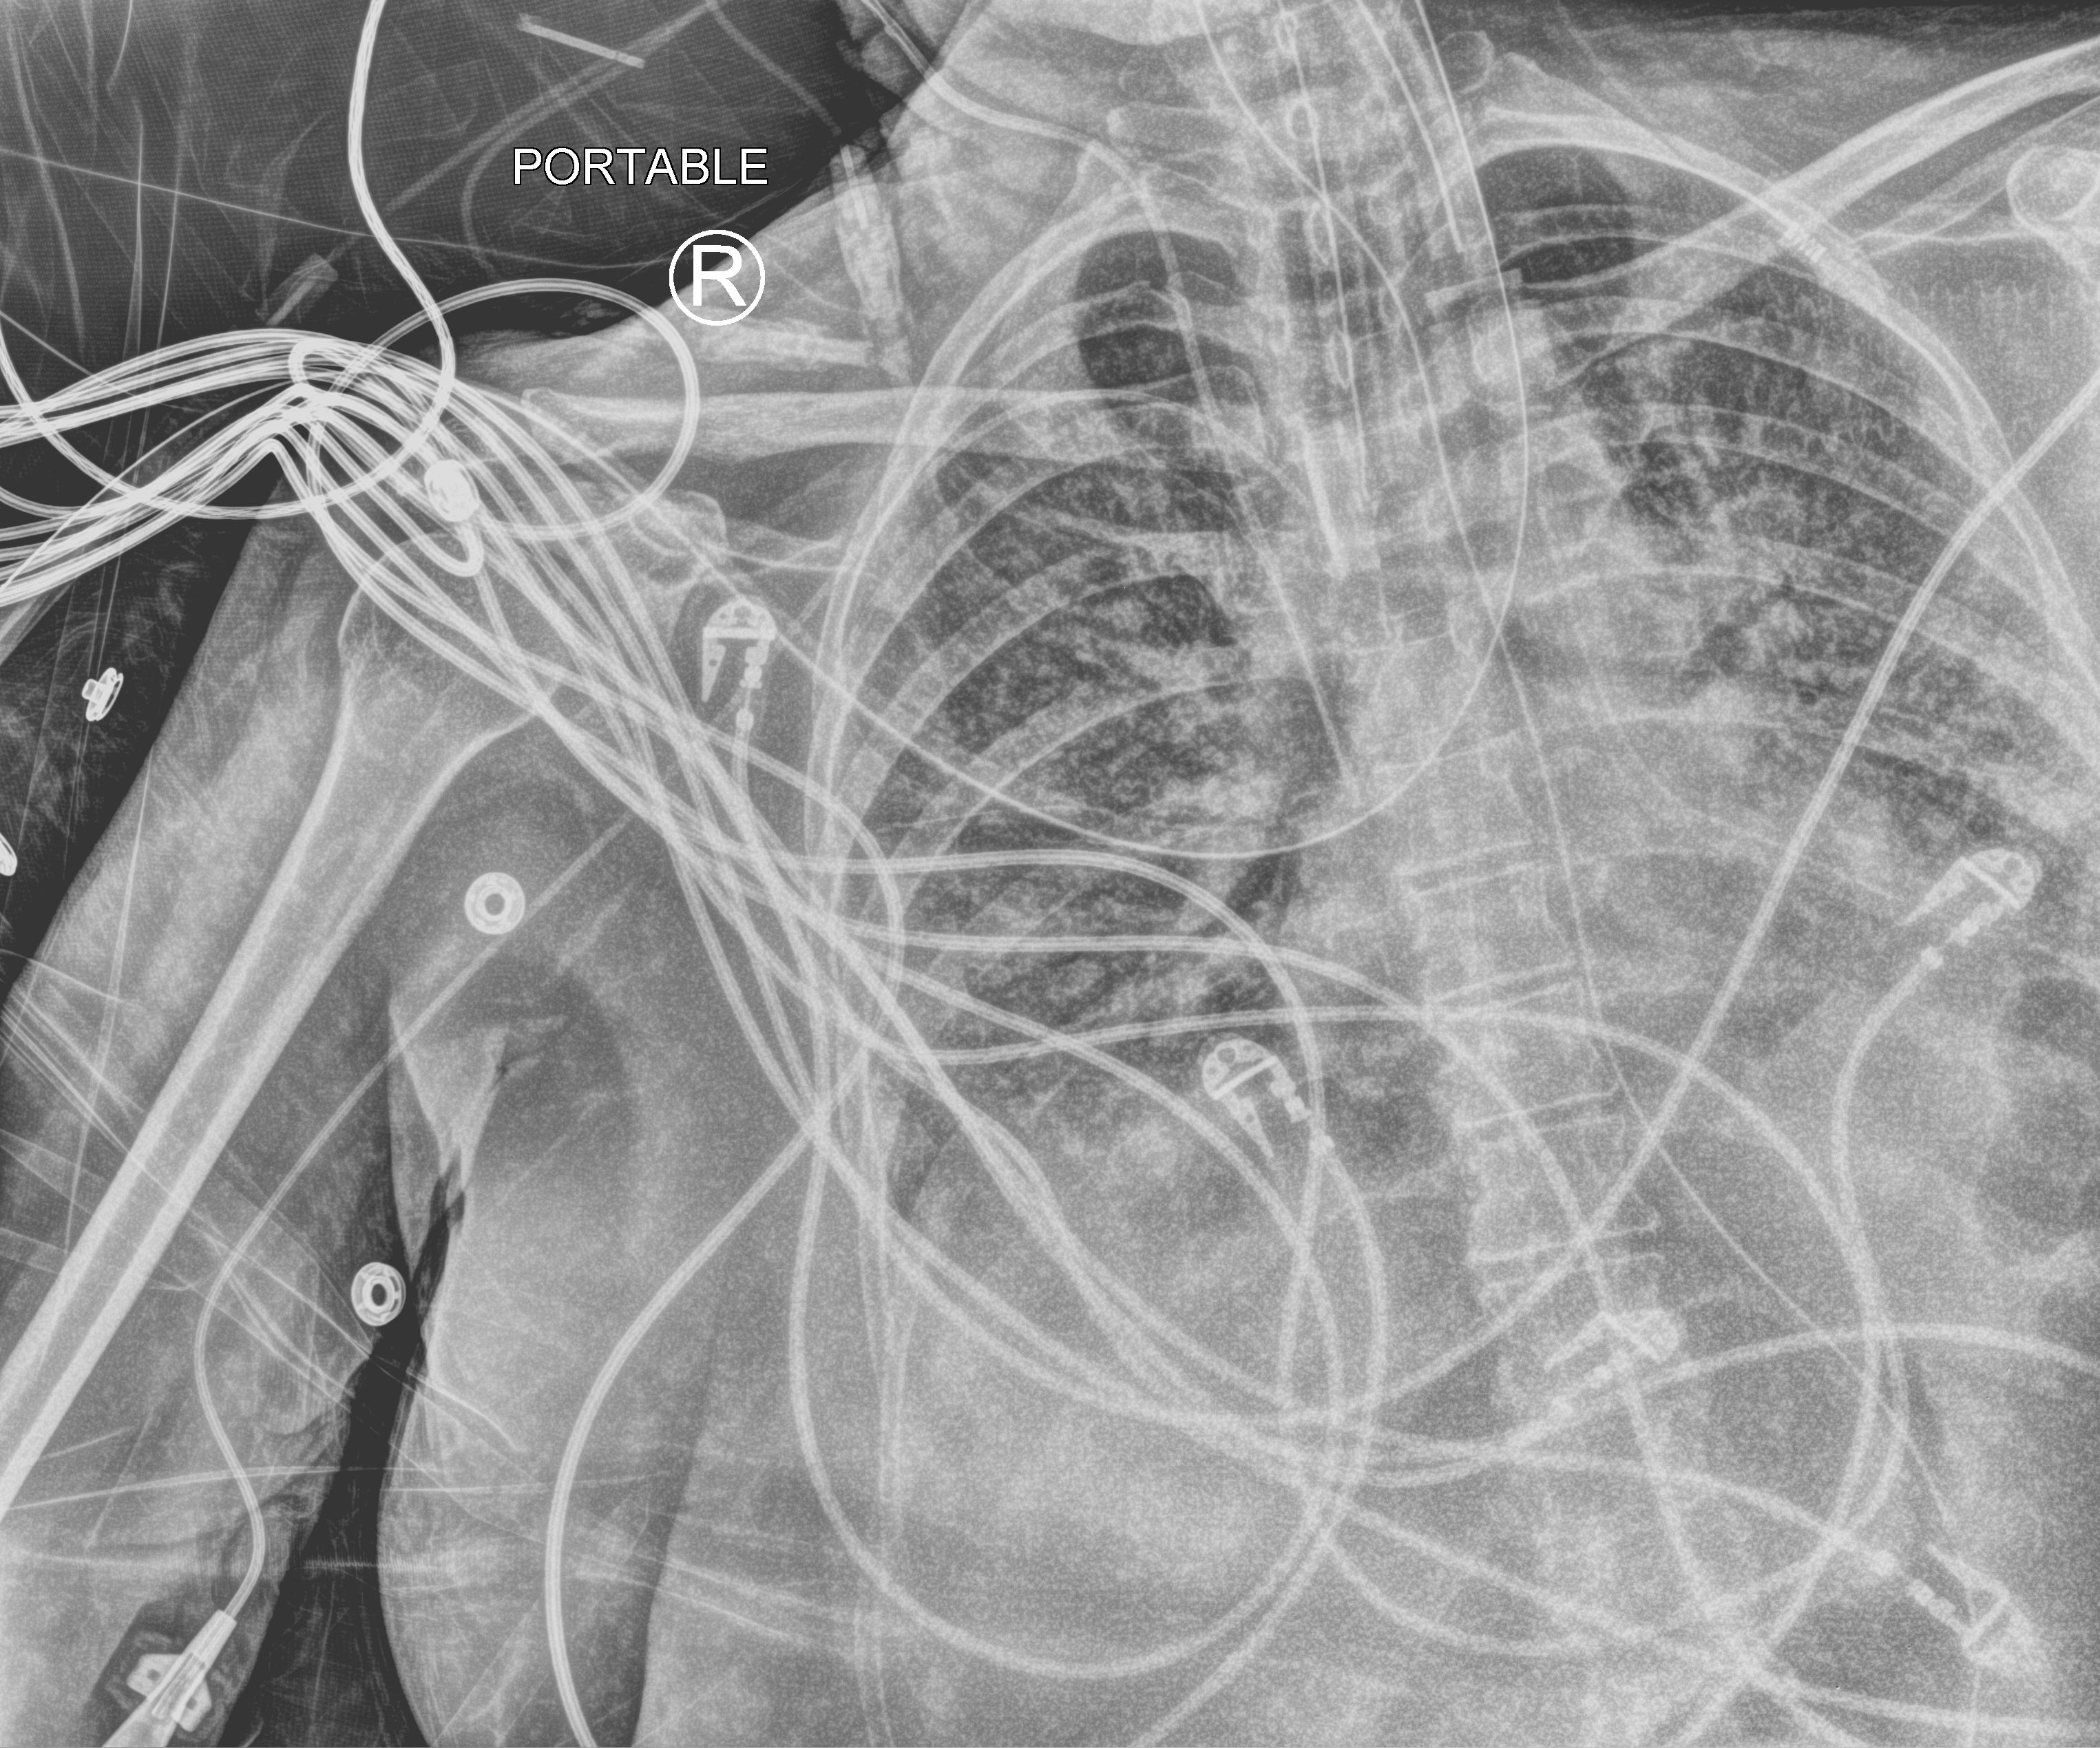
Chest X-ray (portable); anteroposterior (AP) projection. Patient hospitalised with COVID-19; female, aged 60–74 years.
Hospital-stay facts (about this admission, not read from this image; timing relative to this image not recorded): admitted to intensive care during this hospital stay: yes.